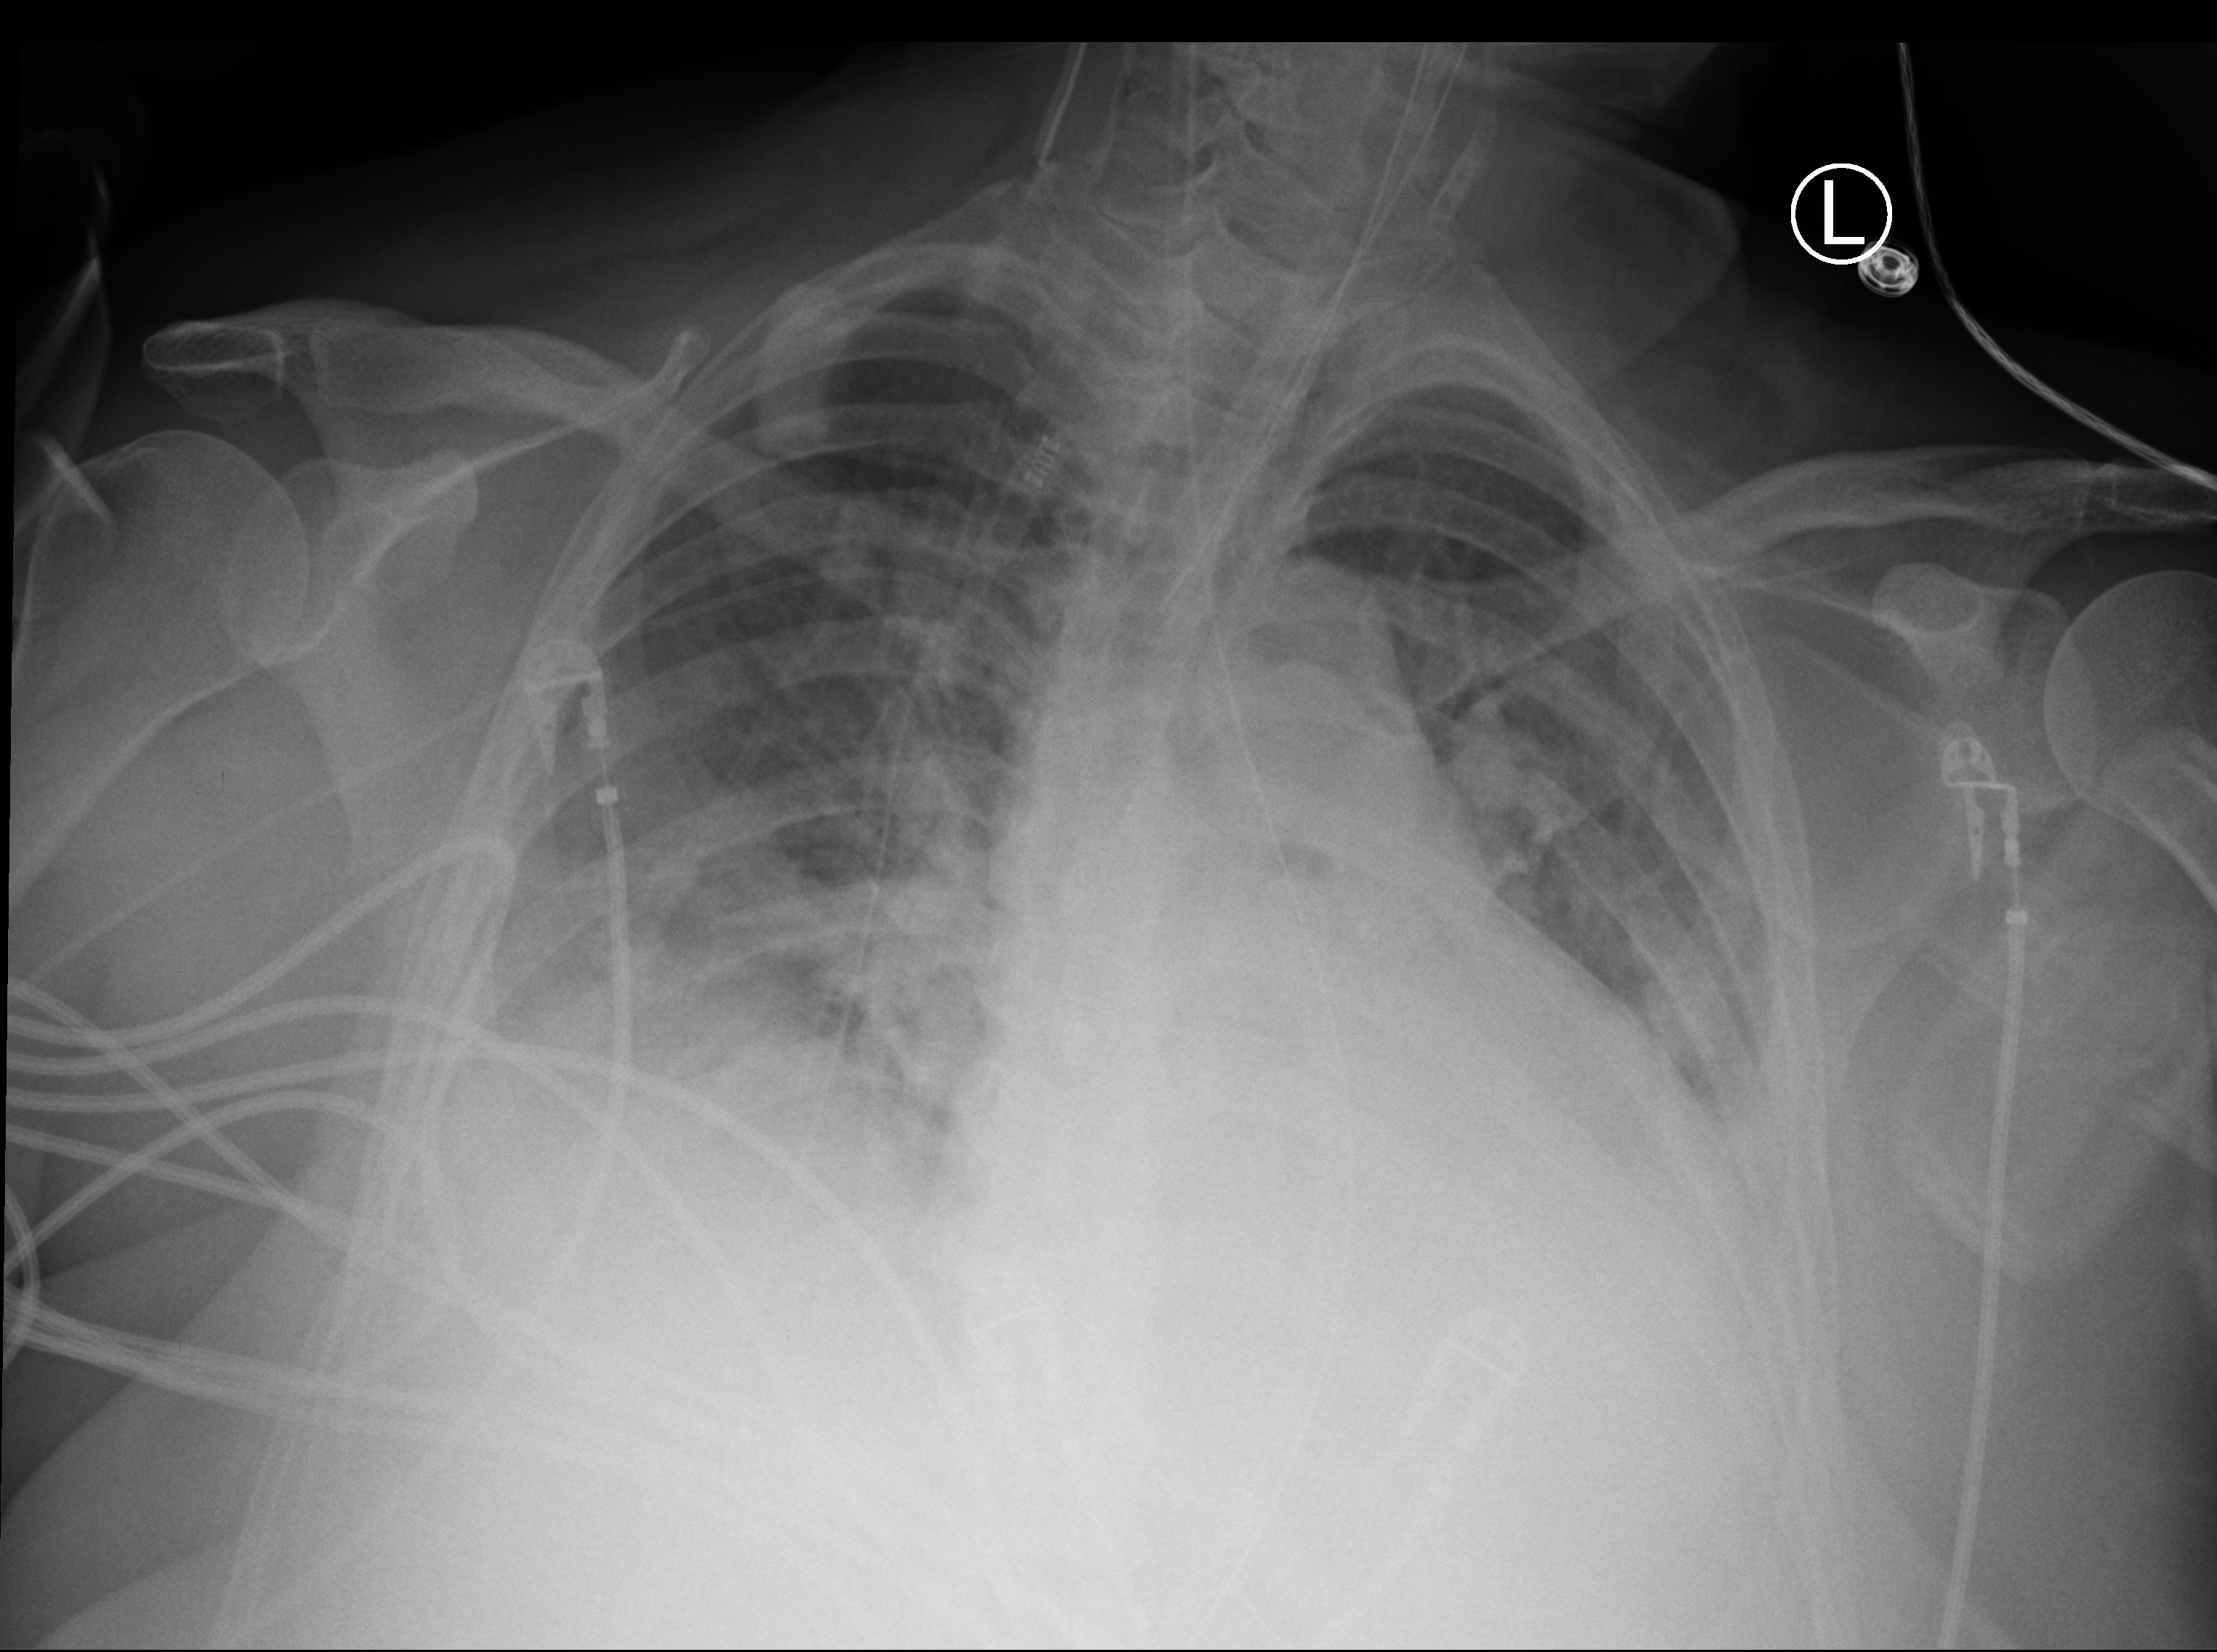
Bedside chest radiograph (computed radiography); anteroposterior (AP) projection. Patient hospitalised with COVID-19; female, aged 60–74 years.
From the hospital-stay record, not from the radiograph (when in the stay this image was taken is not recorded): mechanically ventilated during this hospital stay: yes.